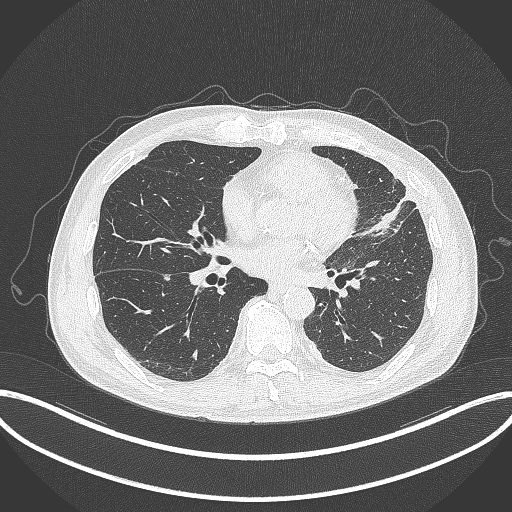
Chest CT, one axial slice. Position 146 of 382 along the scan axis. Reconstruction kernel B70f. Lung window (W 1500 / L -600 HU). 1 mm slice thickness. 512 × 512 image matrix, field of view 415 × 415 mm. Patient: male, 64 years. Case-level facts recorded for this patient, not image findings: clinical TNM (as recorded): T4 N1 M0; histopathological grade: G3.
Structures marked on this image (bounding box drawn by a radiologist):
- lung tumour (recorded histology: adenocarcinoma): bounding box [x1, y1, x2, y2] px = [358, 190, 412, 239]